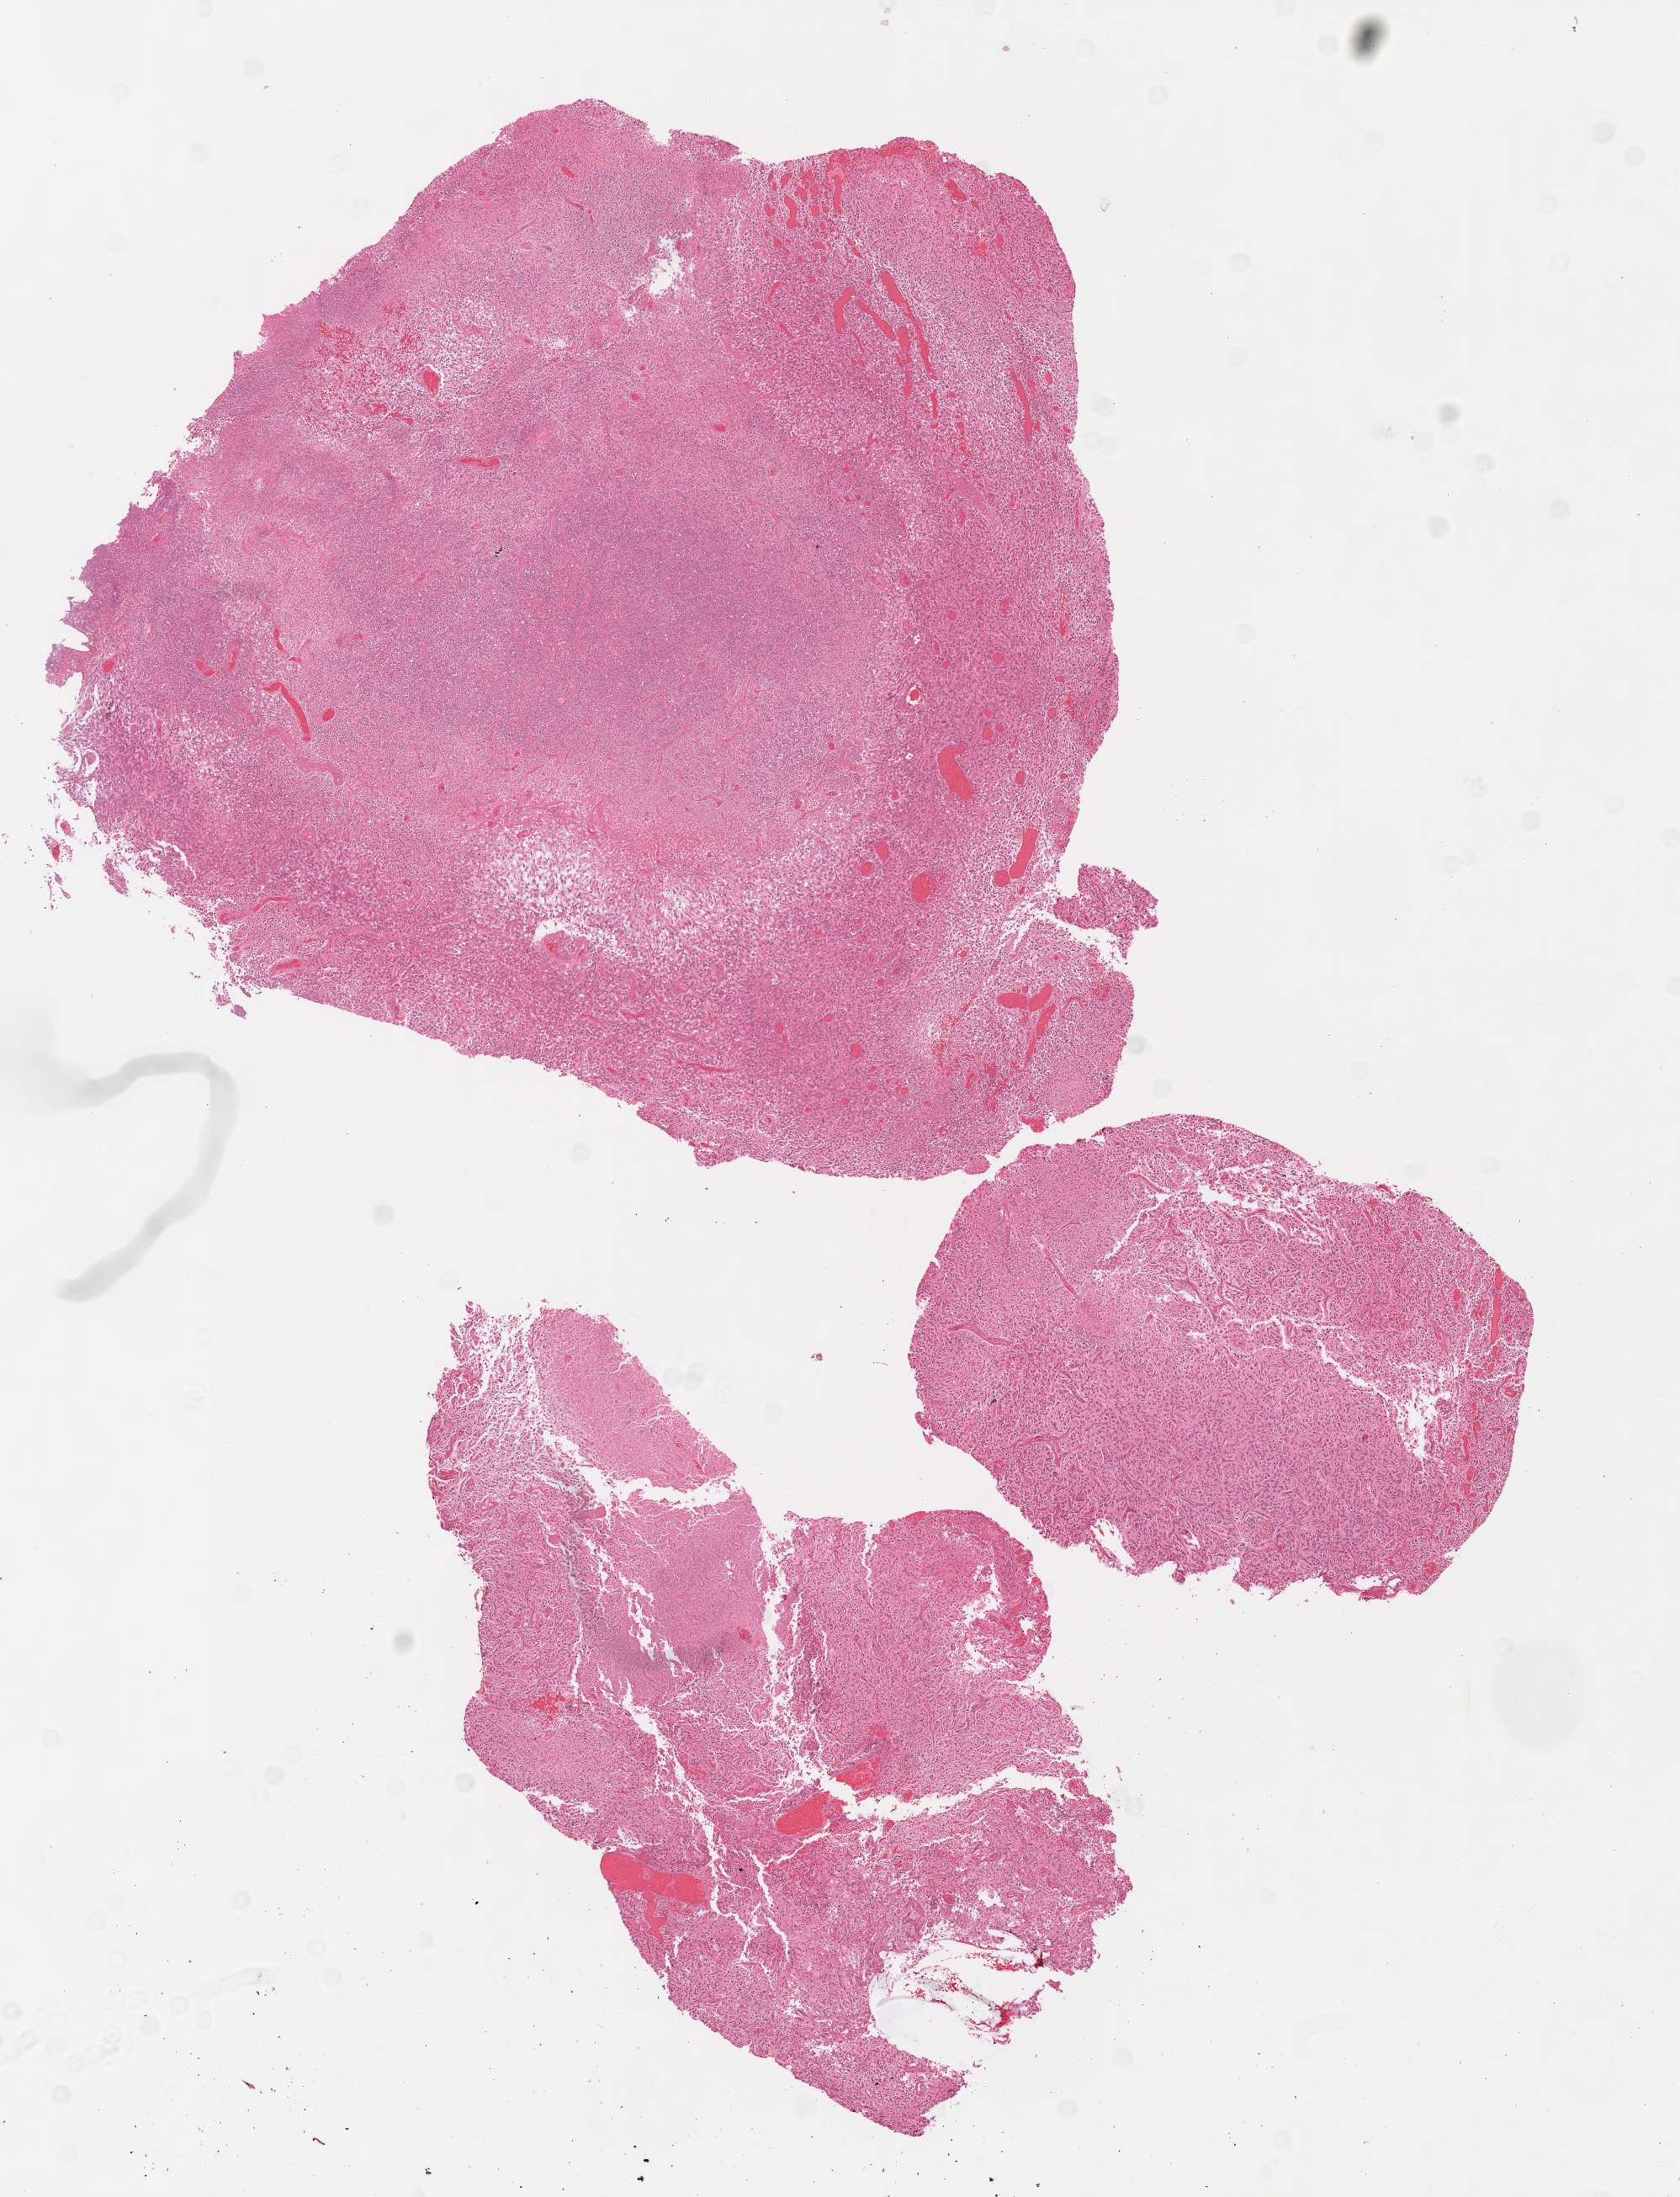
Digitized H&E tissue section (whole slide) — shown as a low-resolution overview of the whole scanned area (about 8.0 x 10.4 mm, from a 20x scan), formalin-fixed paraffin-embedded (FFPE) diagnostic section, sample: primary tumour, brain. Male patient; age at initial diagnosis 68 years.
Pathologic diagnosis: Glioblastoma.